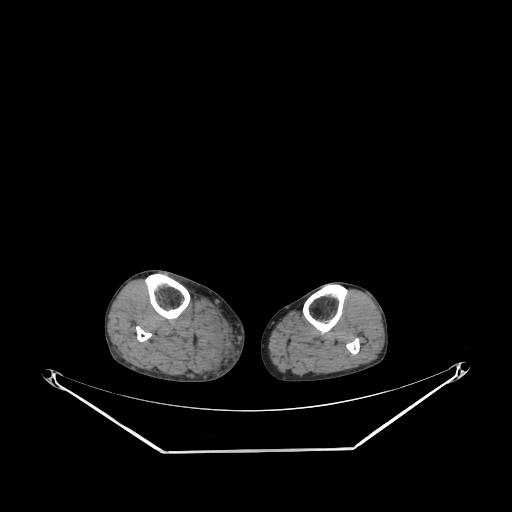
CT of an extremity soft-tissue mass (from a PET/CT study), one axial slice; position 148 of 267 along the scan axis; reconstruction kernel SOFT; 140 kVp; soft-tissue window (W 400 / L 40 HU); 3.75 mm slice thickness; 512 × 512 image matrix, field of view 500 × 500 mm. Male patient. From the clinical record (not read from this slice): histological type: pleiomorphic liposarcoma; grade: high; site of the primary tumour: right calf.
Annotated regions visible in this slice (expert contour drawn on MRI and transferred to this co-registered scan by the dataset authors):
- gross tumour volume including surrounding oedema: box from (x=222, y=324) to (x=227, y=334) px